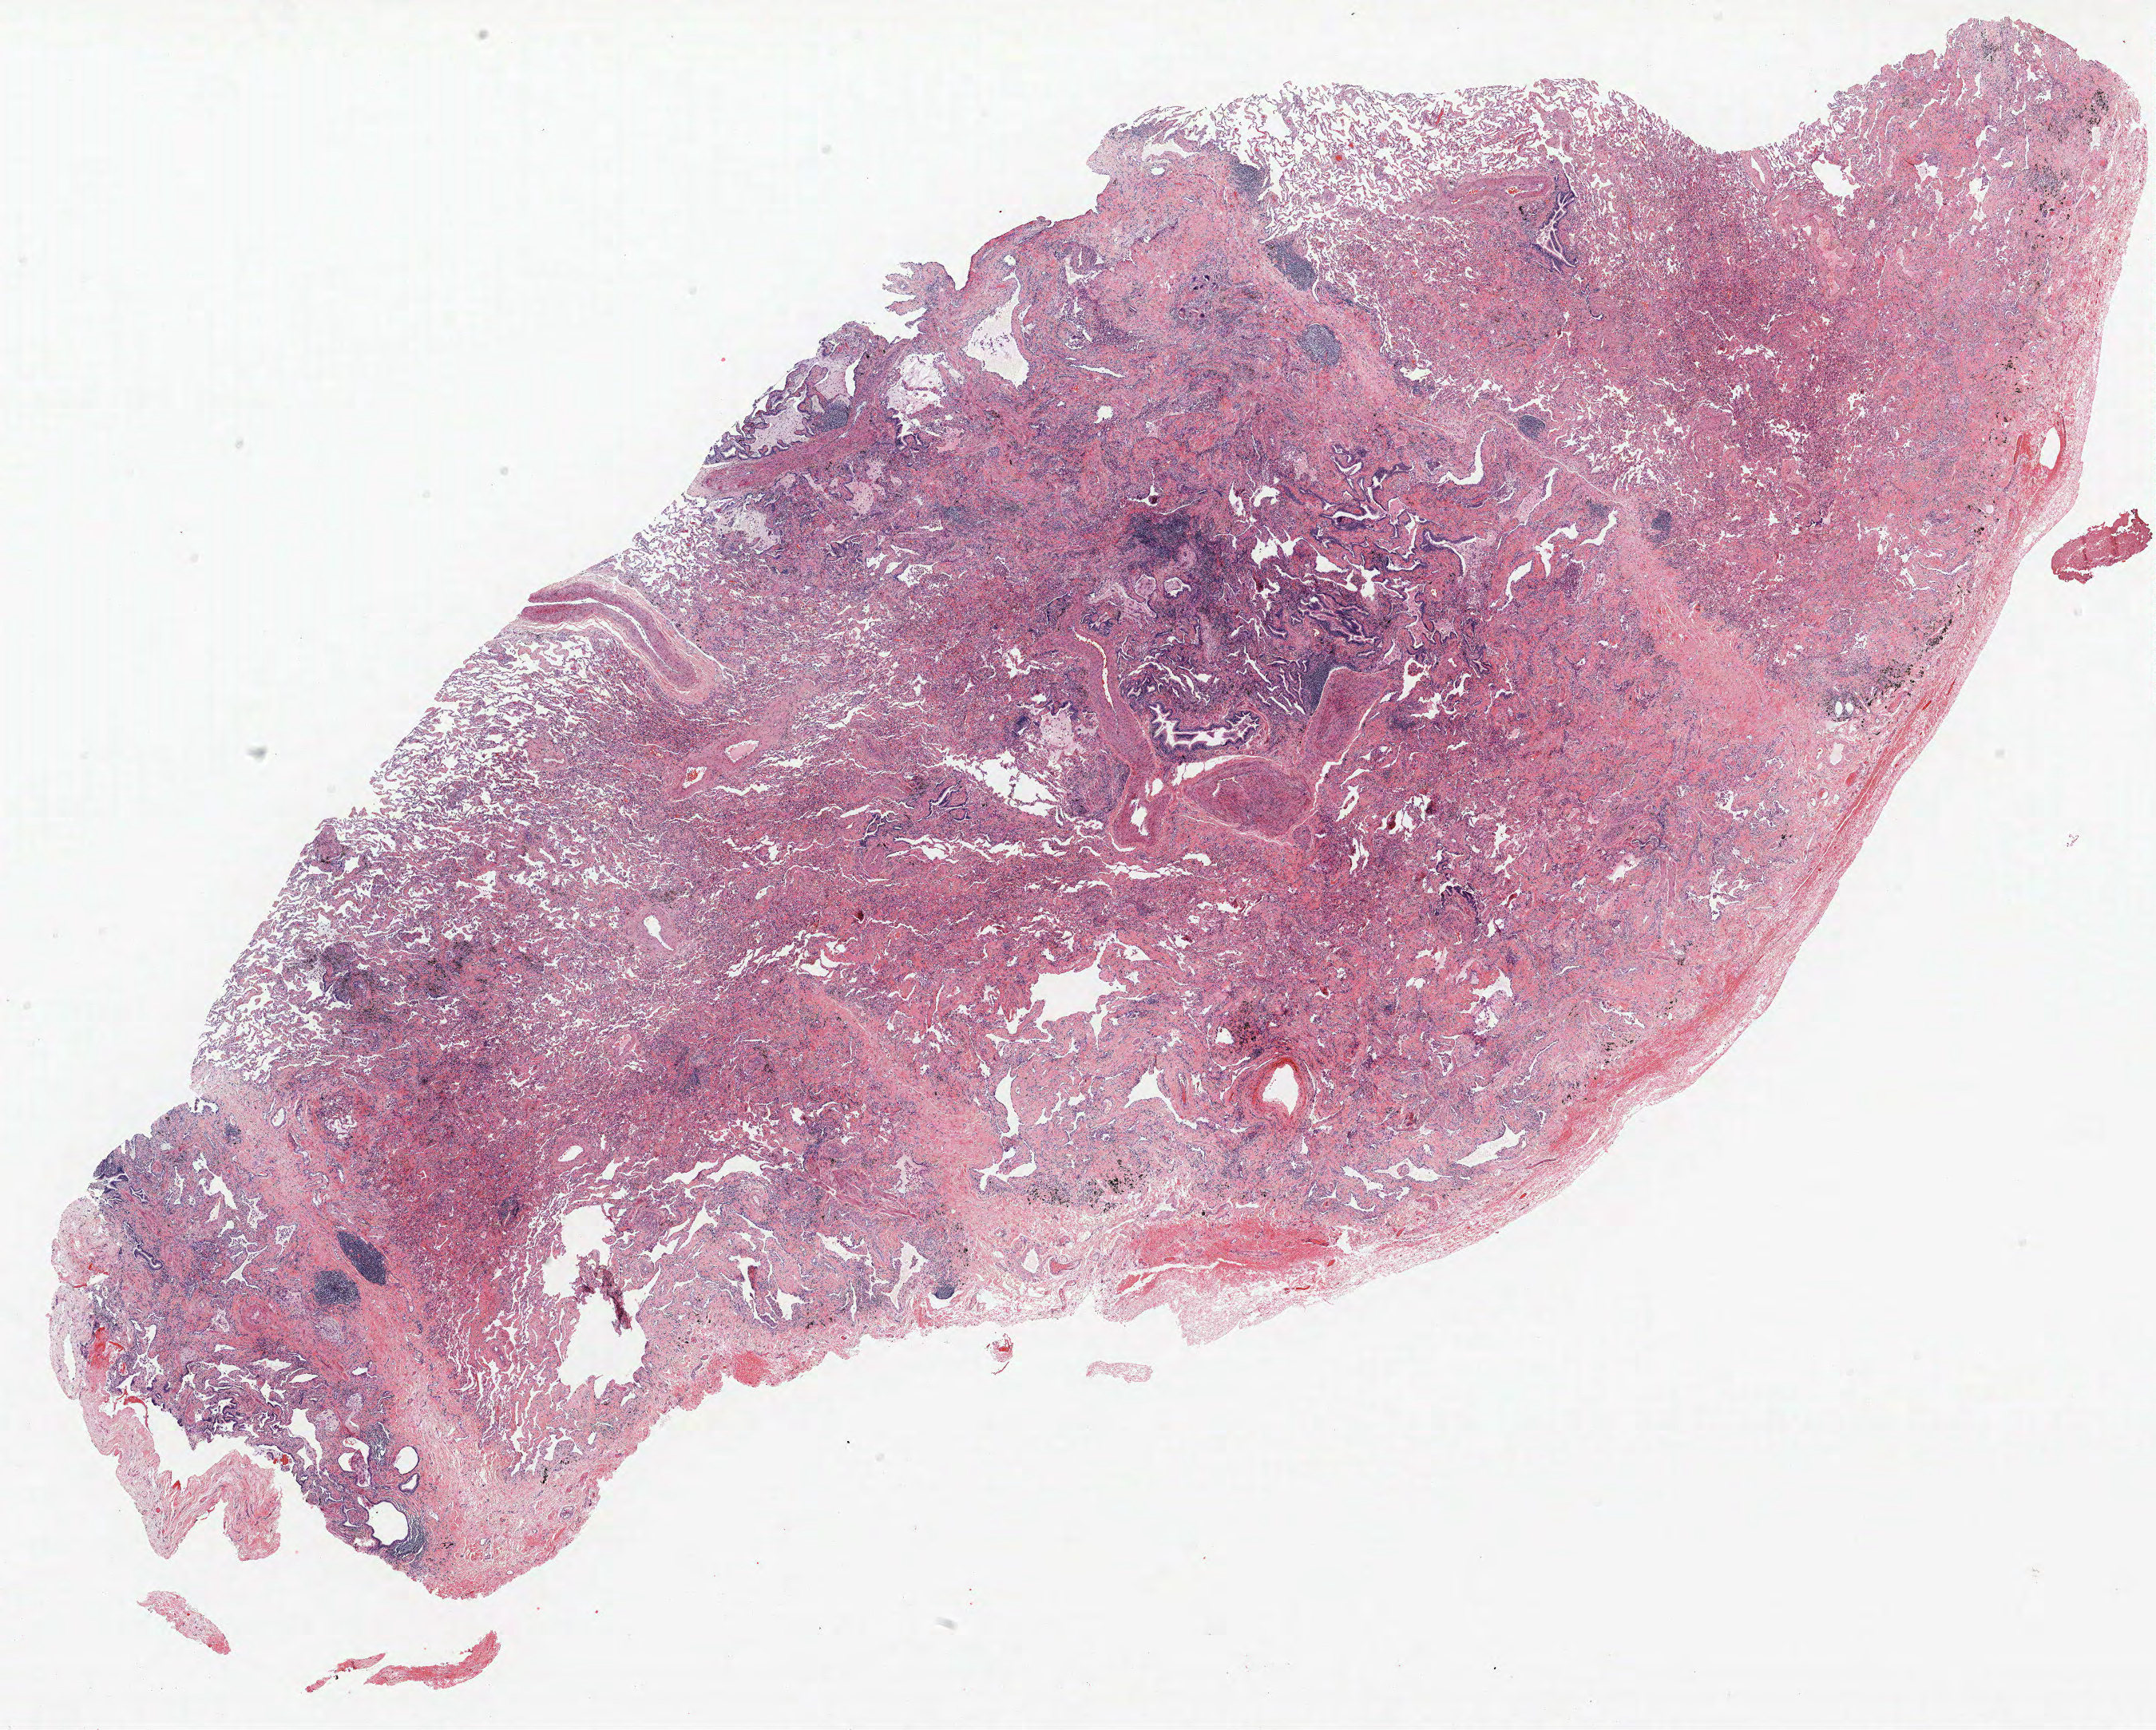
Whole-slide histology image, H&E-stained — low-resolution overview of the scanned area, about 21.6 x 17.3 mm (slide scanned at 40x); formalin-fixed paraffin-embedded (FFPE) section; lung tissue. Male patient, aged 59 at enrolment. Grade: moderately differentiated (G2).
• stage (AJCC 6th edition): IA
• primary tumour location (clinical record): right upper lobe, right middle lobe
• ICD-O-3 topography: lung, NOS (C34.9)
• participant's lung-cancer diagnosis: Adenocarcinoma, NOS (ICD-O-3 8140/3)
• tumour size (pathology): 13 mm
• note: participant had 2 primary lung cancers recorded; fields above describe the first